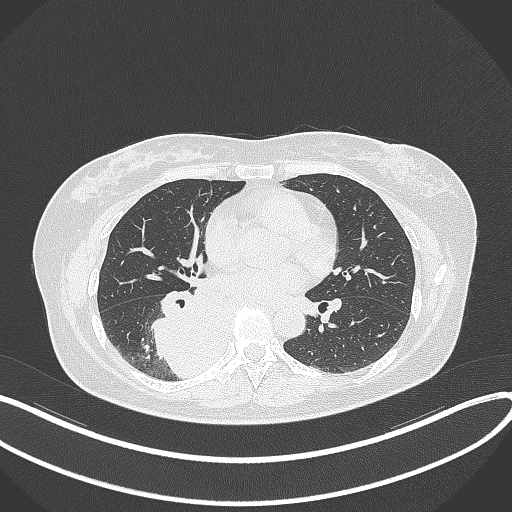
Chest CT, one axial slice; slice 169 of 331 in the series (ordered by position); 120 kVp; lung window (W 1500 / L -600 HU); 1 mm slice thickness; 512 × 512 image matrix, field of view 400 × 400 mm. Patient: female, 54 years. From the clinical record (not read from this slice): clinical TNM (as recorded): T4 N0 M0.
Structures marked on this image (bounding box drawn by a radiologist):
- lung tumour (recorded histology: adenocarcinoma): bounding box [x1, y1, x2, y2] px = [148, 285, 224, 382]